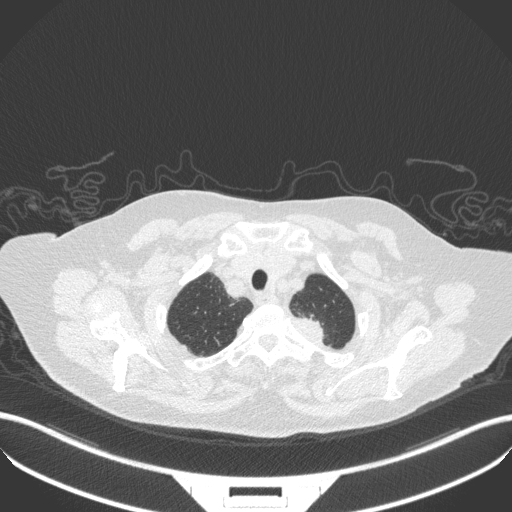
Chest CT, one axial slice; slice 308 of 353 in the series (ordered by position); lung window (W 1500 / L -600 HU); 1 mm slice thickness; 512 × 512 image matrix. Female patient, age 81 years. Case-level facts recorded for this patient, not image findings: clinical TNM (as recorded): T2a N0 M0.
Annotated regions visible in this slice (bounding box drawn by a radiologist):
- lung tumour (recorded histology: adenocarcinoma): bounding box [x1, y1, x2, y2] px = [295, 315, 334, 345]